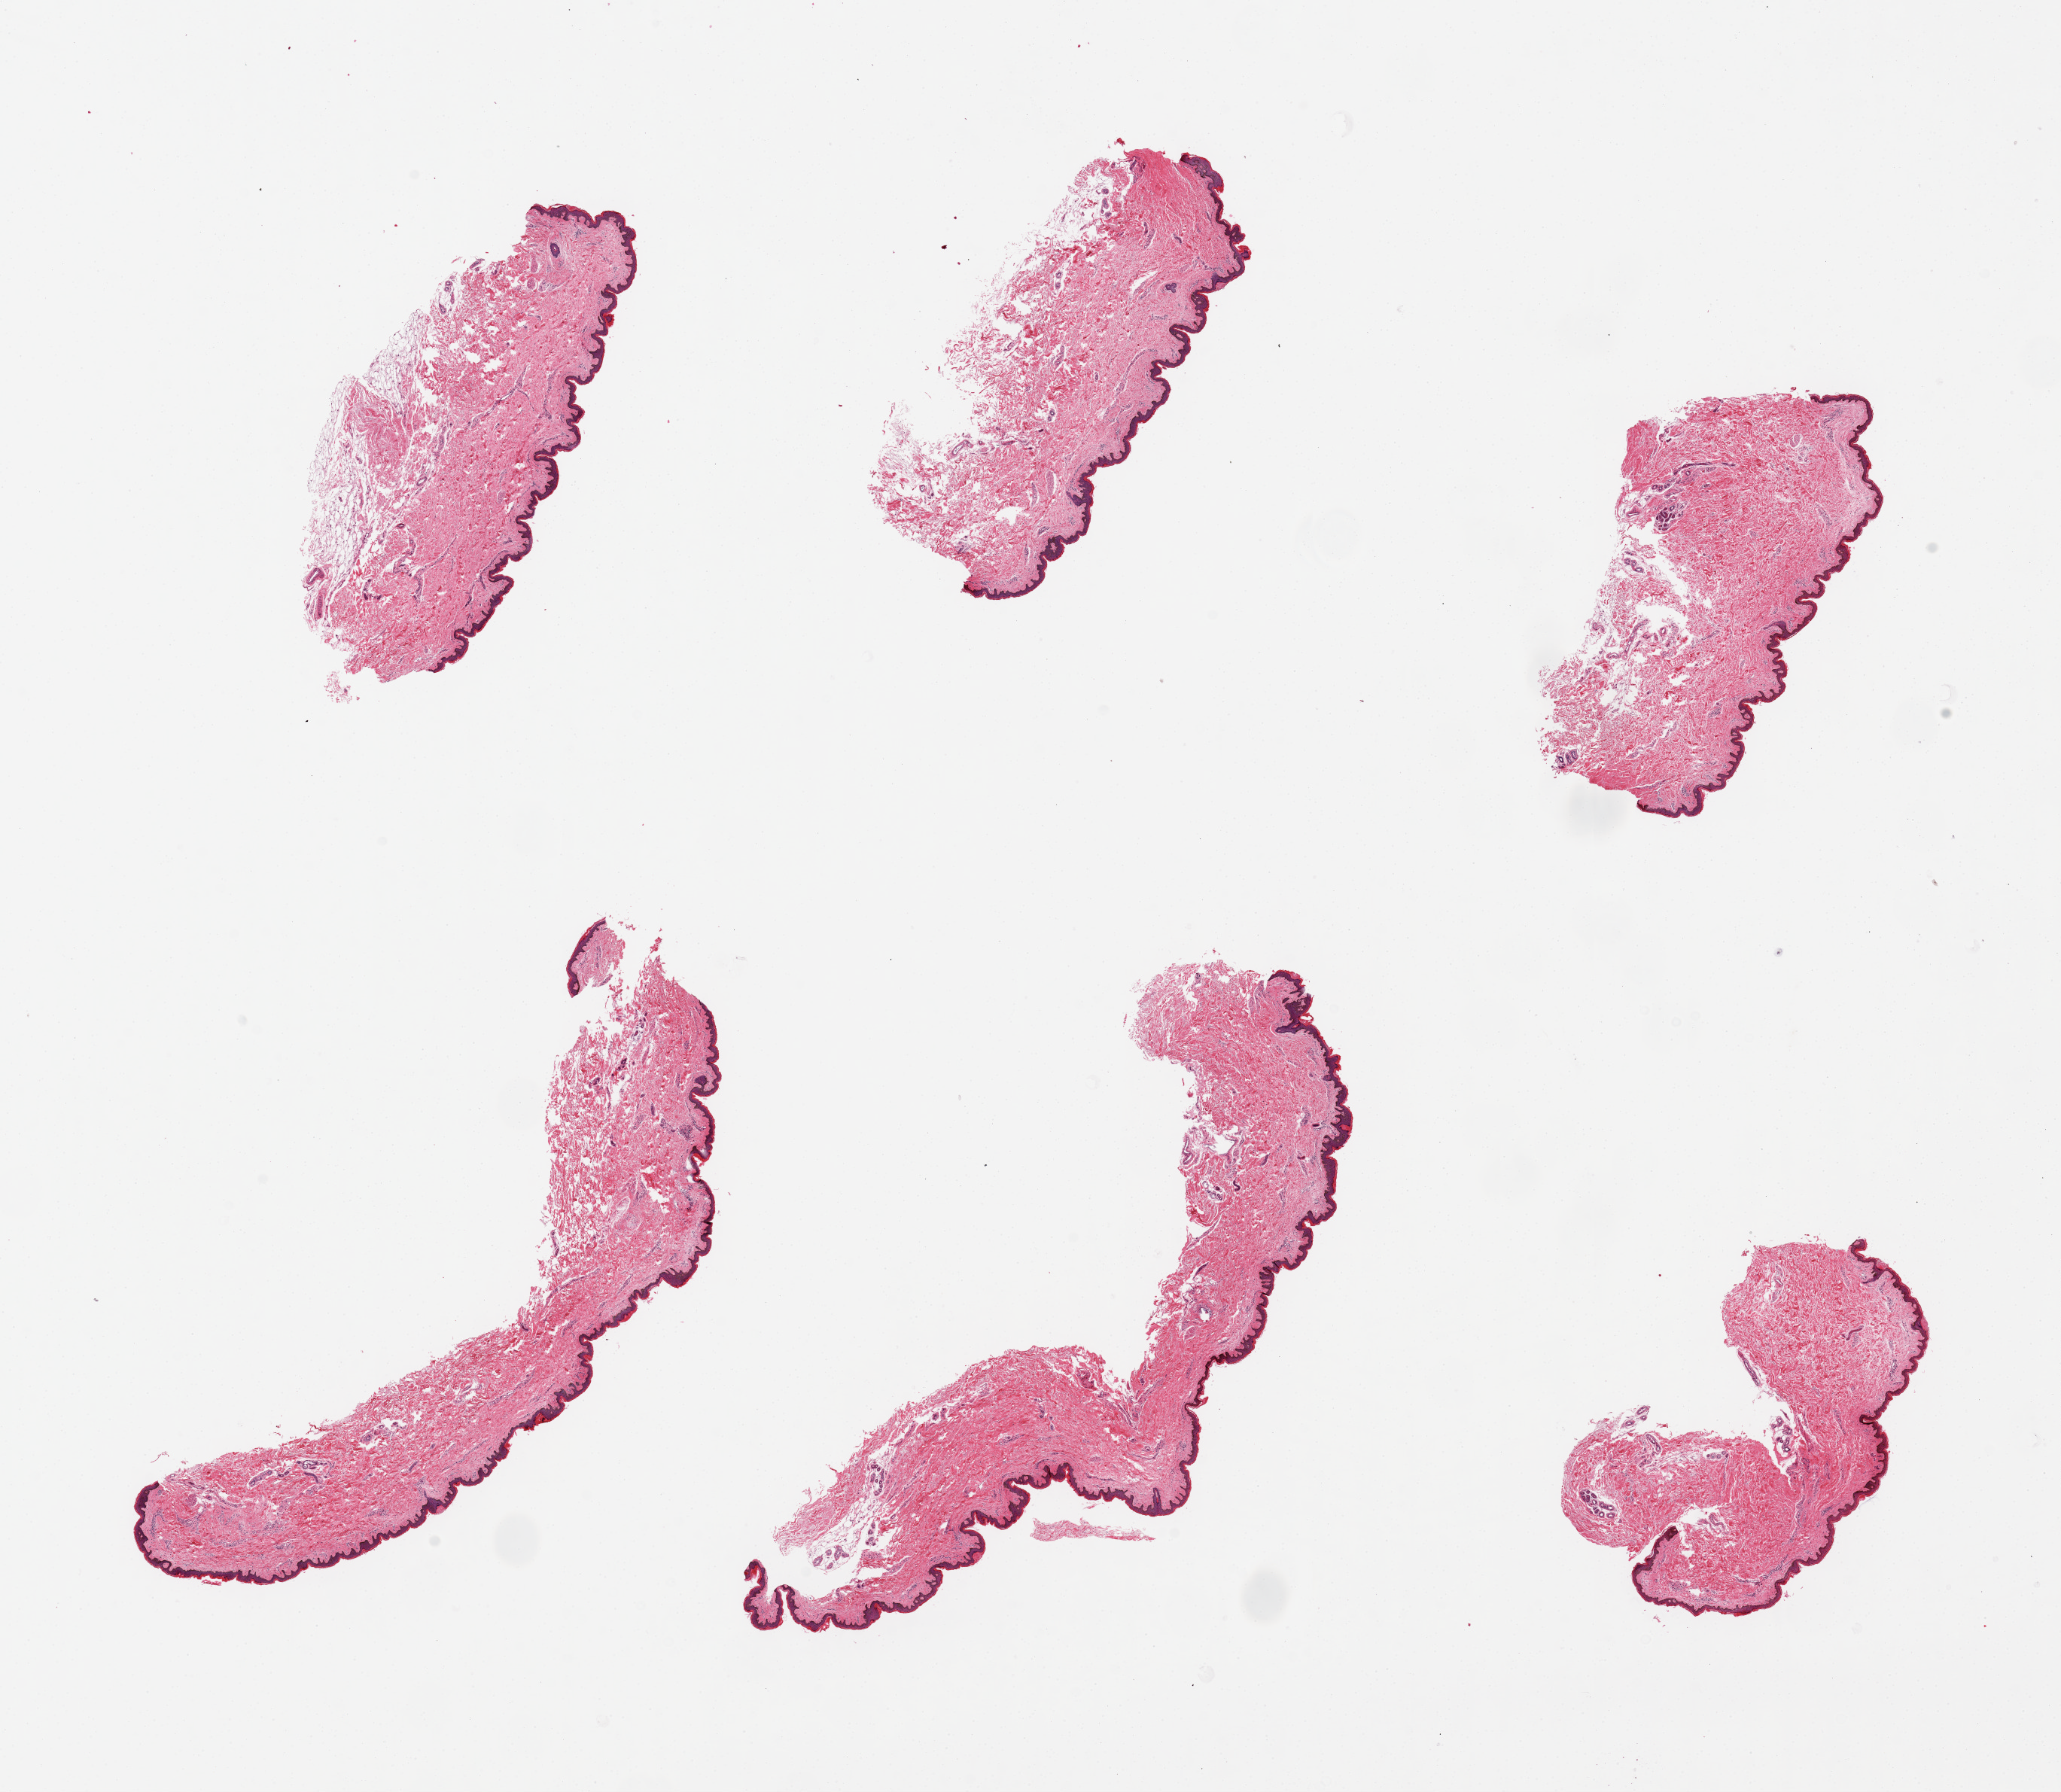
Whole-slide image, H&E stain, a low-resolution overview of the entire scanned area, about 21.7 x 18.8 mm (from a 20x scan); PAXgene-fixed paraffin-embedded (PFPE) section; target tissue: skin of lower leg; donor tissue sample. Female donor.
• review note (as recorded): 6 pieces, up to 9x3.5mm; squamous epithelium is ~3% ofthickness